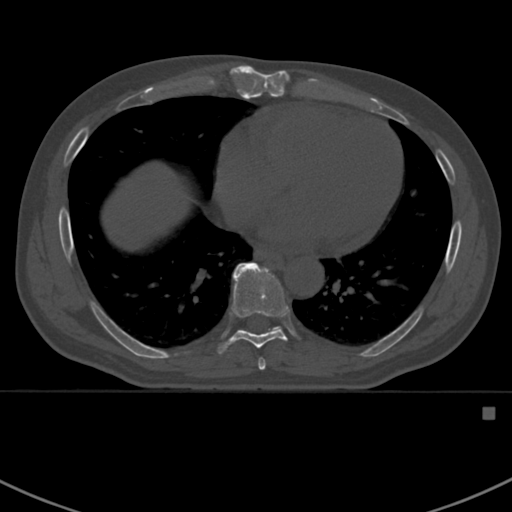
CT including the spine, one axial slice. Position 398 of 412 along the scan axis. 120 kVp. Bone window (W 1800 / L 400 HU). 1.5 mm slice thickness. 512 × 512 image matrix. Male patient, age 59 years. Case-level facts recorded for this patient, not image findings: primary cancer: prostate.
Structures marked on this image (semi-automatic segmentation, software-assisted and operator-edited):
- T7 vertebra: bounding box <258,359,266,370> (left, top, right, bottom; pixels)
- T8 vertebra: <217,263,287,353>
- T9 vertebra: <232,262,284,331>